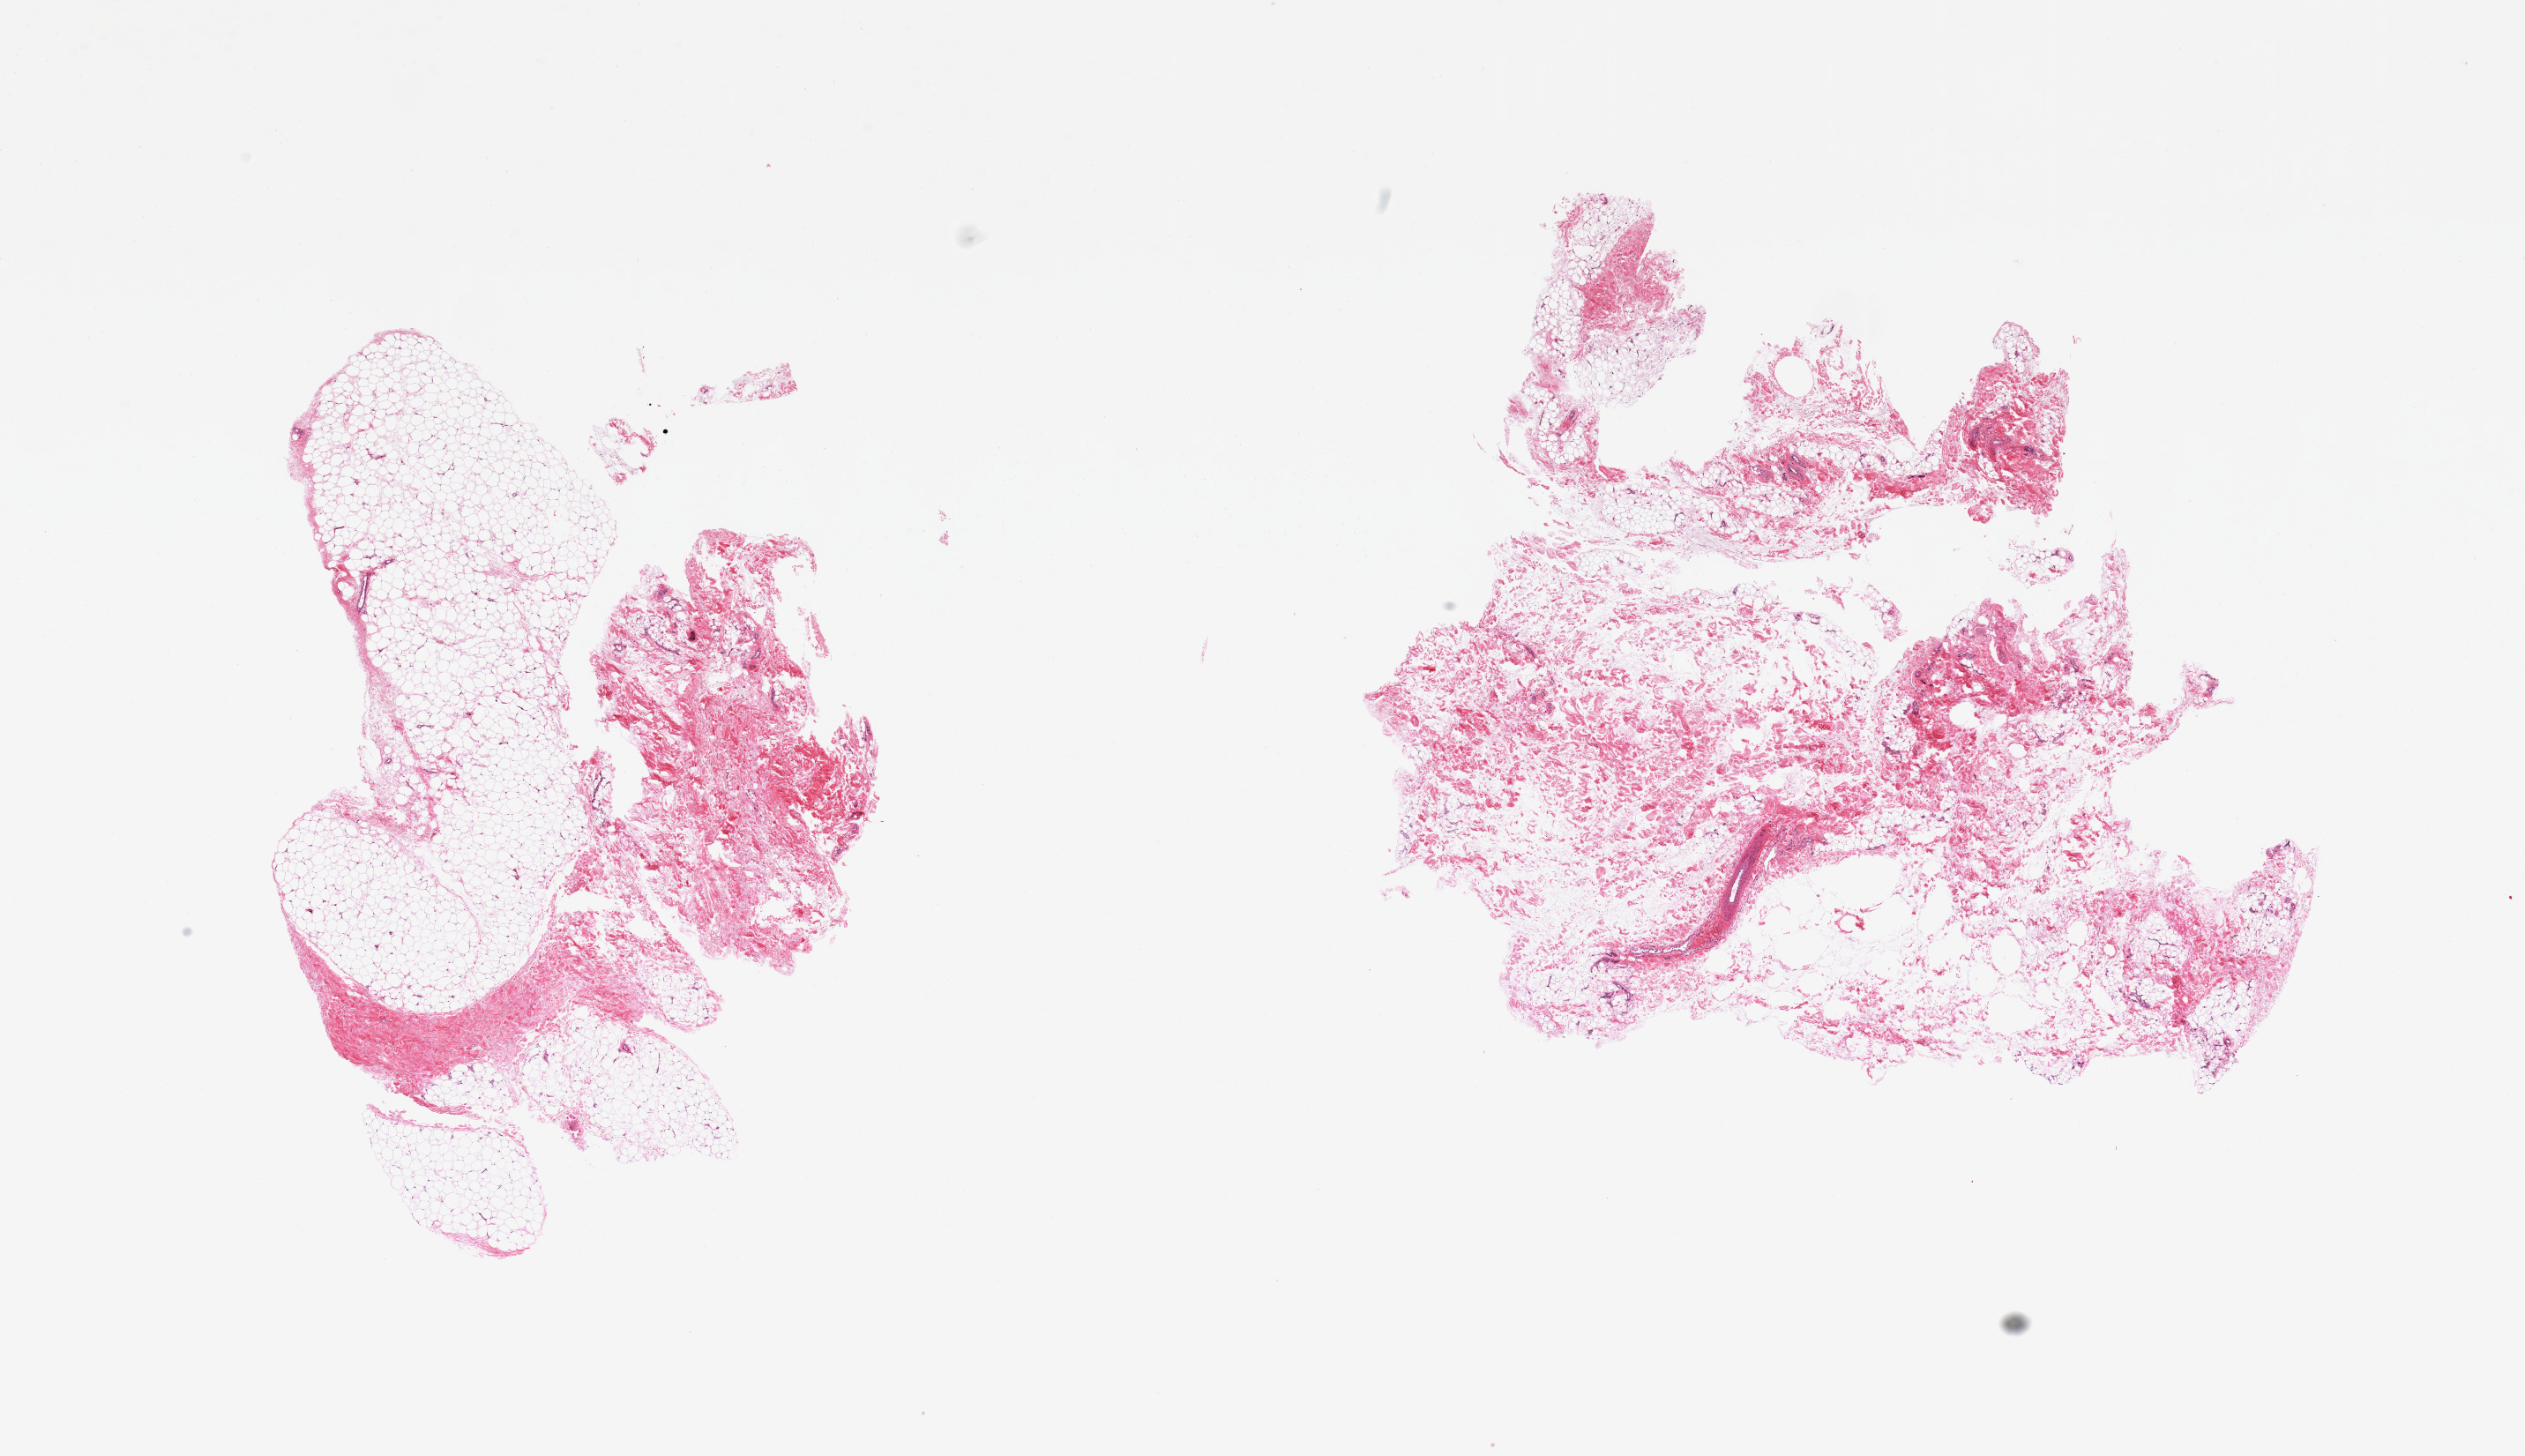
Digitized hematoxylin and eosin (H&E)-stained section, shown as a low-resolution overview of the whole scanned area (about 22.6 x 13.1 mm), PAXgene-fixed paraffin-embedded (PFPE) section, section of adipose tissue (target tissue), tissue donor sample. Donor: male.
Pathologist's review note for this sample: 2 pieces, ~40% fascia, sample carefully.